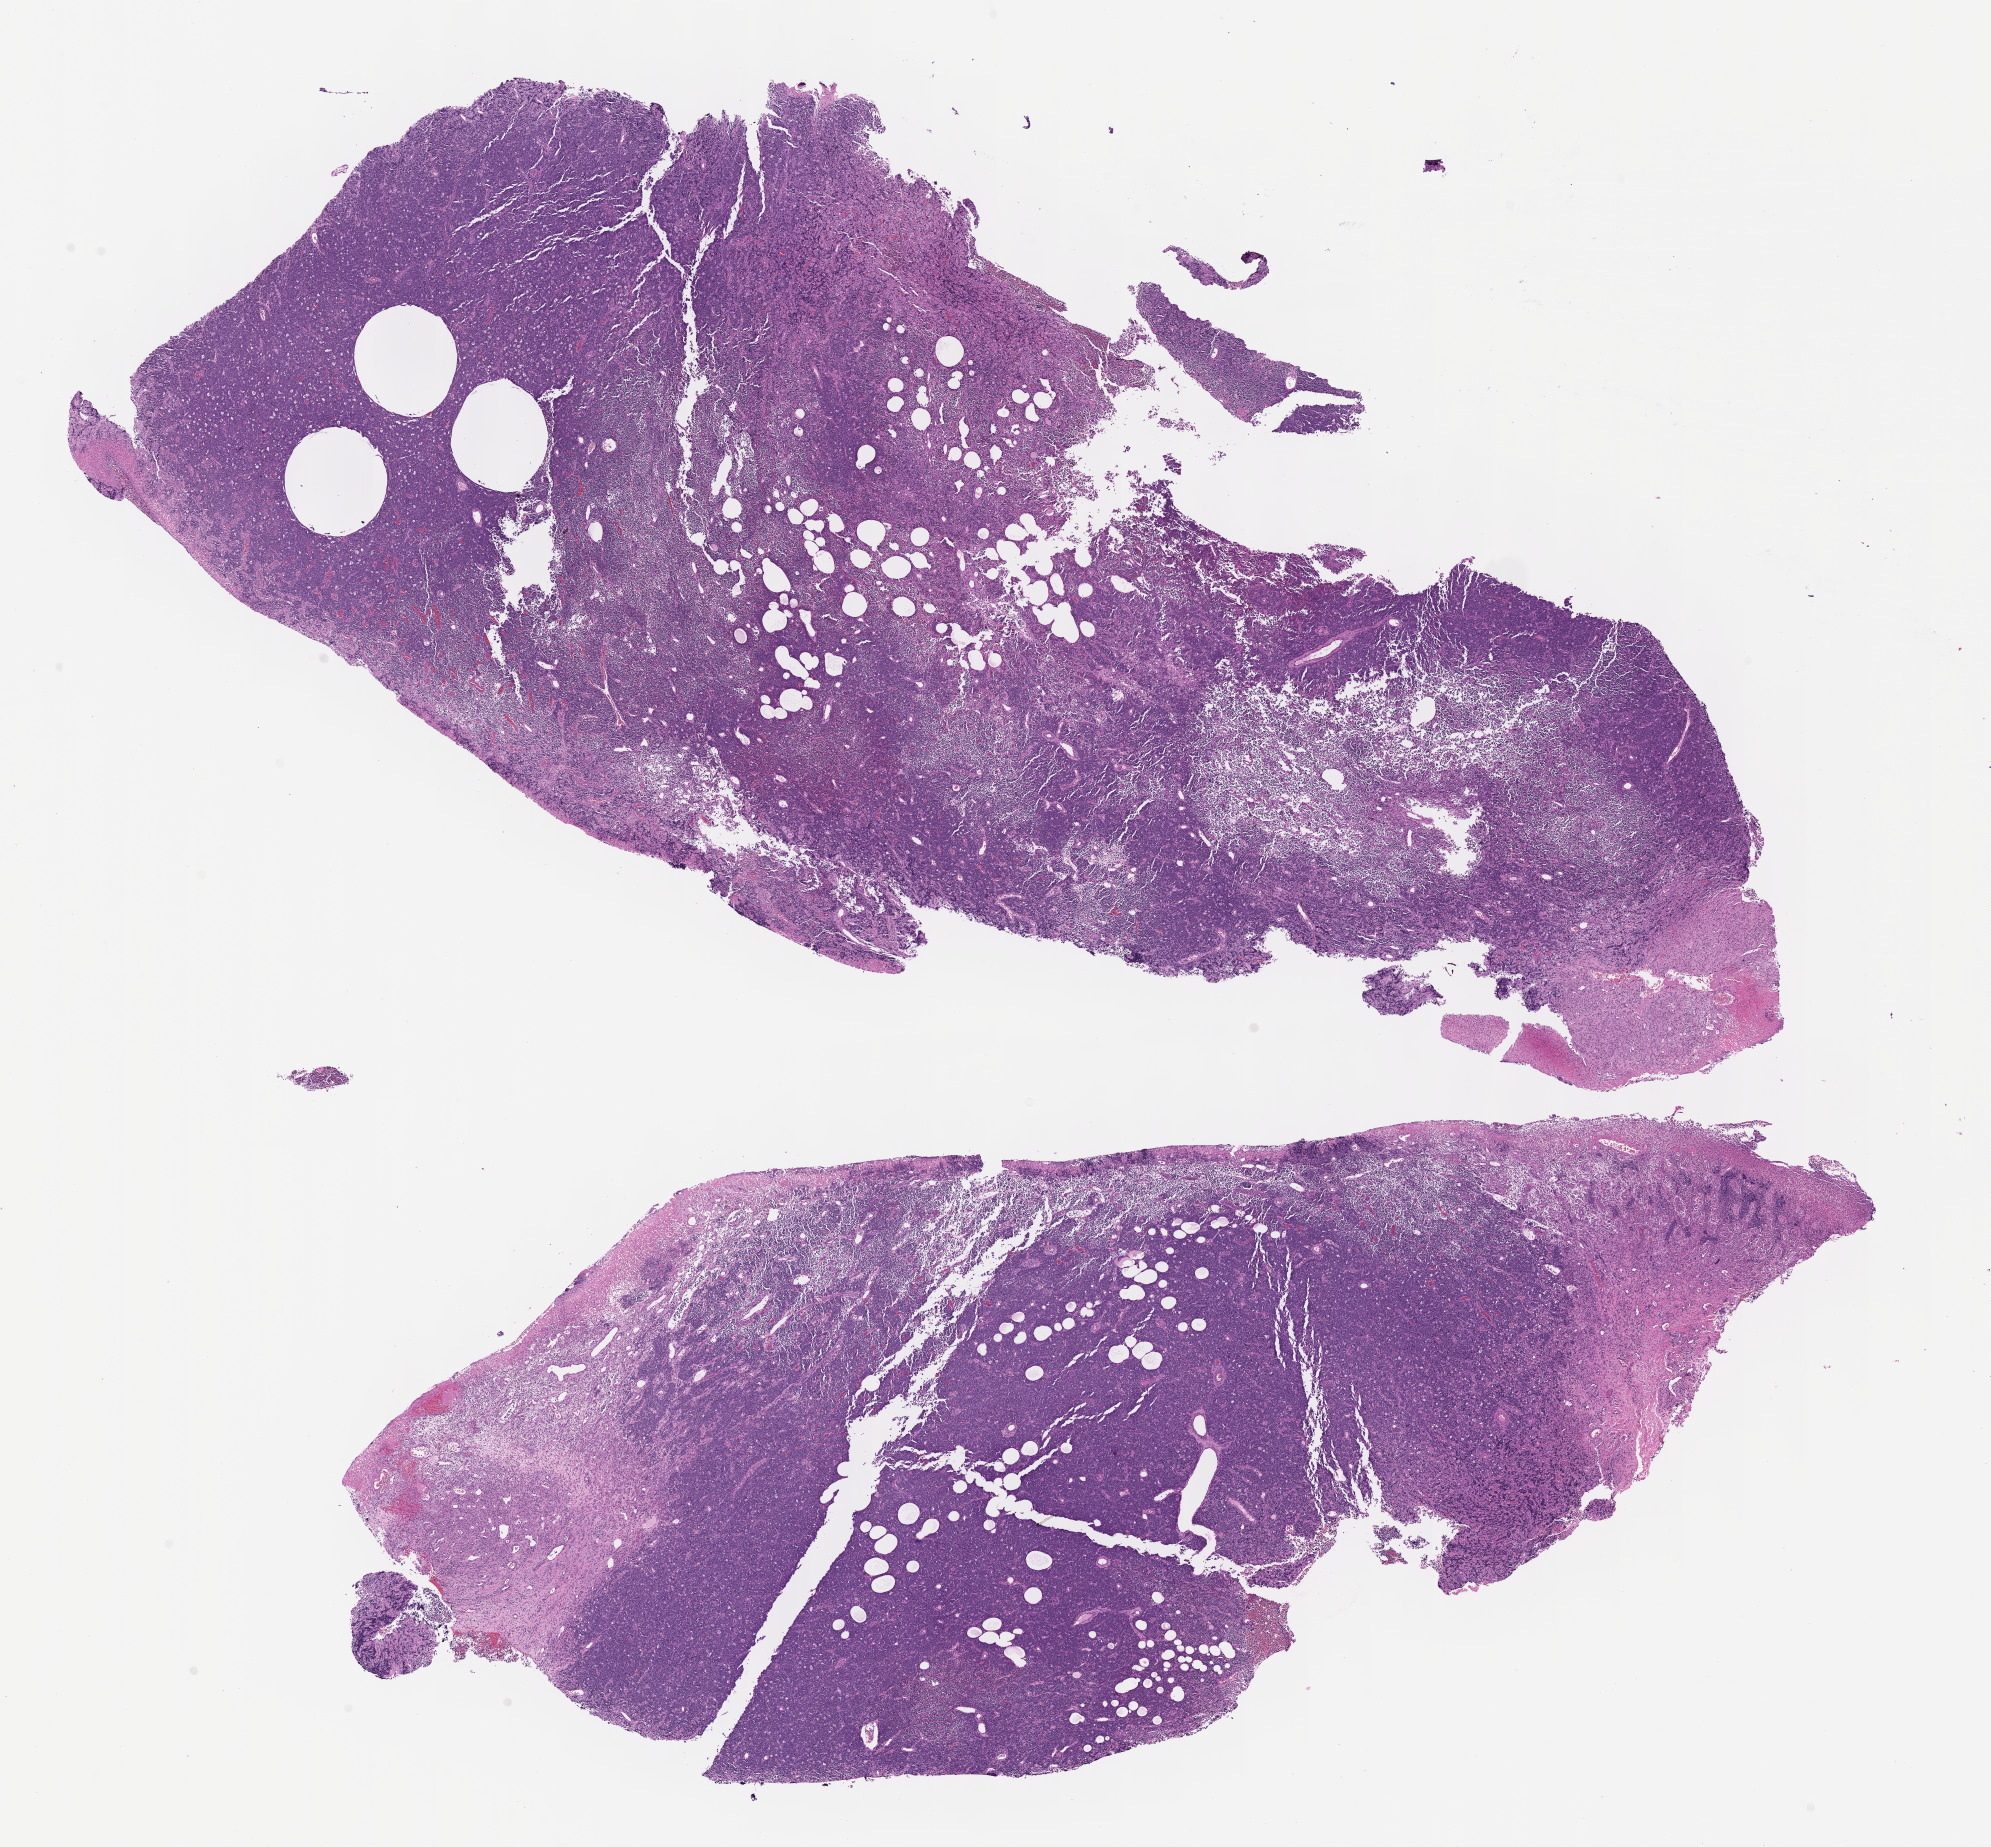
Digitized haematoxylin and eosin-stained section — low-resolution overview of the scanned area, about 16.1 x 14.9 mm; FFPE section; primary tumor; site: cranium. Patient: female, age at initial diagnosis 6 years. Slide review estimates, as recorded: tumor cells 75%, tumor nuclei 90%, stromal cells 5%, necrosis 10%, normal cells 10%. Infiltration values recorded for this section: lymphocyte infiltration 40%, monocyte infiltration 30%, neutrophil infiltration 5%.
Ann Arbor stage (patient): Stage III. Diagnosis: Burkitt lymphoma, NOS.